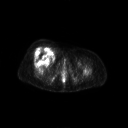
FDG PET of an extremity soft-tissue mass (from a PET/CT study), one axial slice; position 54 of 267 along the scan axis; 128 × 128 image matrix, field of view 700 × 700 mm. Female patient, age 56 years. Case-level facts recorded for this patient, not image findings: histological type: malignant solitary fibrous tumor; grade: intermediate; site of the primary tumour: right thigh.
Annotated regions visible in this slice (expert contour drawn on MRI and transferred to this co-registered scan by the dataset authors):
- gross tumour volume including surrounding oedema: box from (x=32, y=46) to (x=54, y=62) px
- gross tumour volume (mass): (x=32, y=47)–(x=53, y=62)